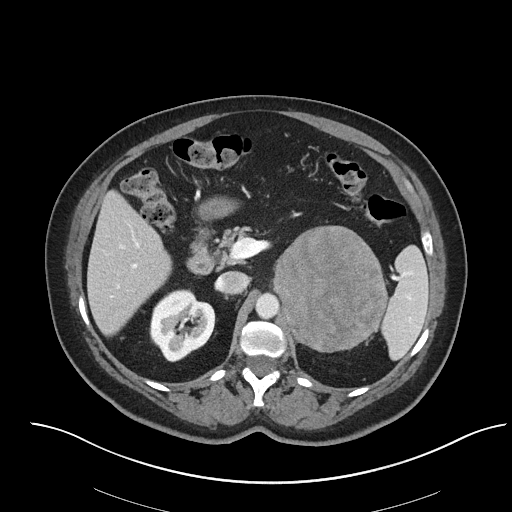
Contrast-enhanced abdominal CT, one axial slice; 120 kVp; soft-tissue window (W 400 / L 40 HU); 512 × 512 image matrix, field of view 440 × 440 mm. Patient: female, 53 years. Case-level facts recorded for this patient, not image findings: diagnosis: adrenocortical carcinoma; tumour side: left adrenal; tumour size at pathology: 9 cm; Ki-67 index: 28 %; stage (as recorded): 2.
Structures marked on this image (semi-automatic segmentation, software-assisted and operator-edited):
- mass: bounding box (x1, y1, x2, y2) in pixels: (275, 228, 386, 350)